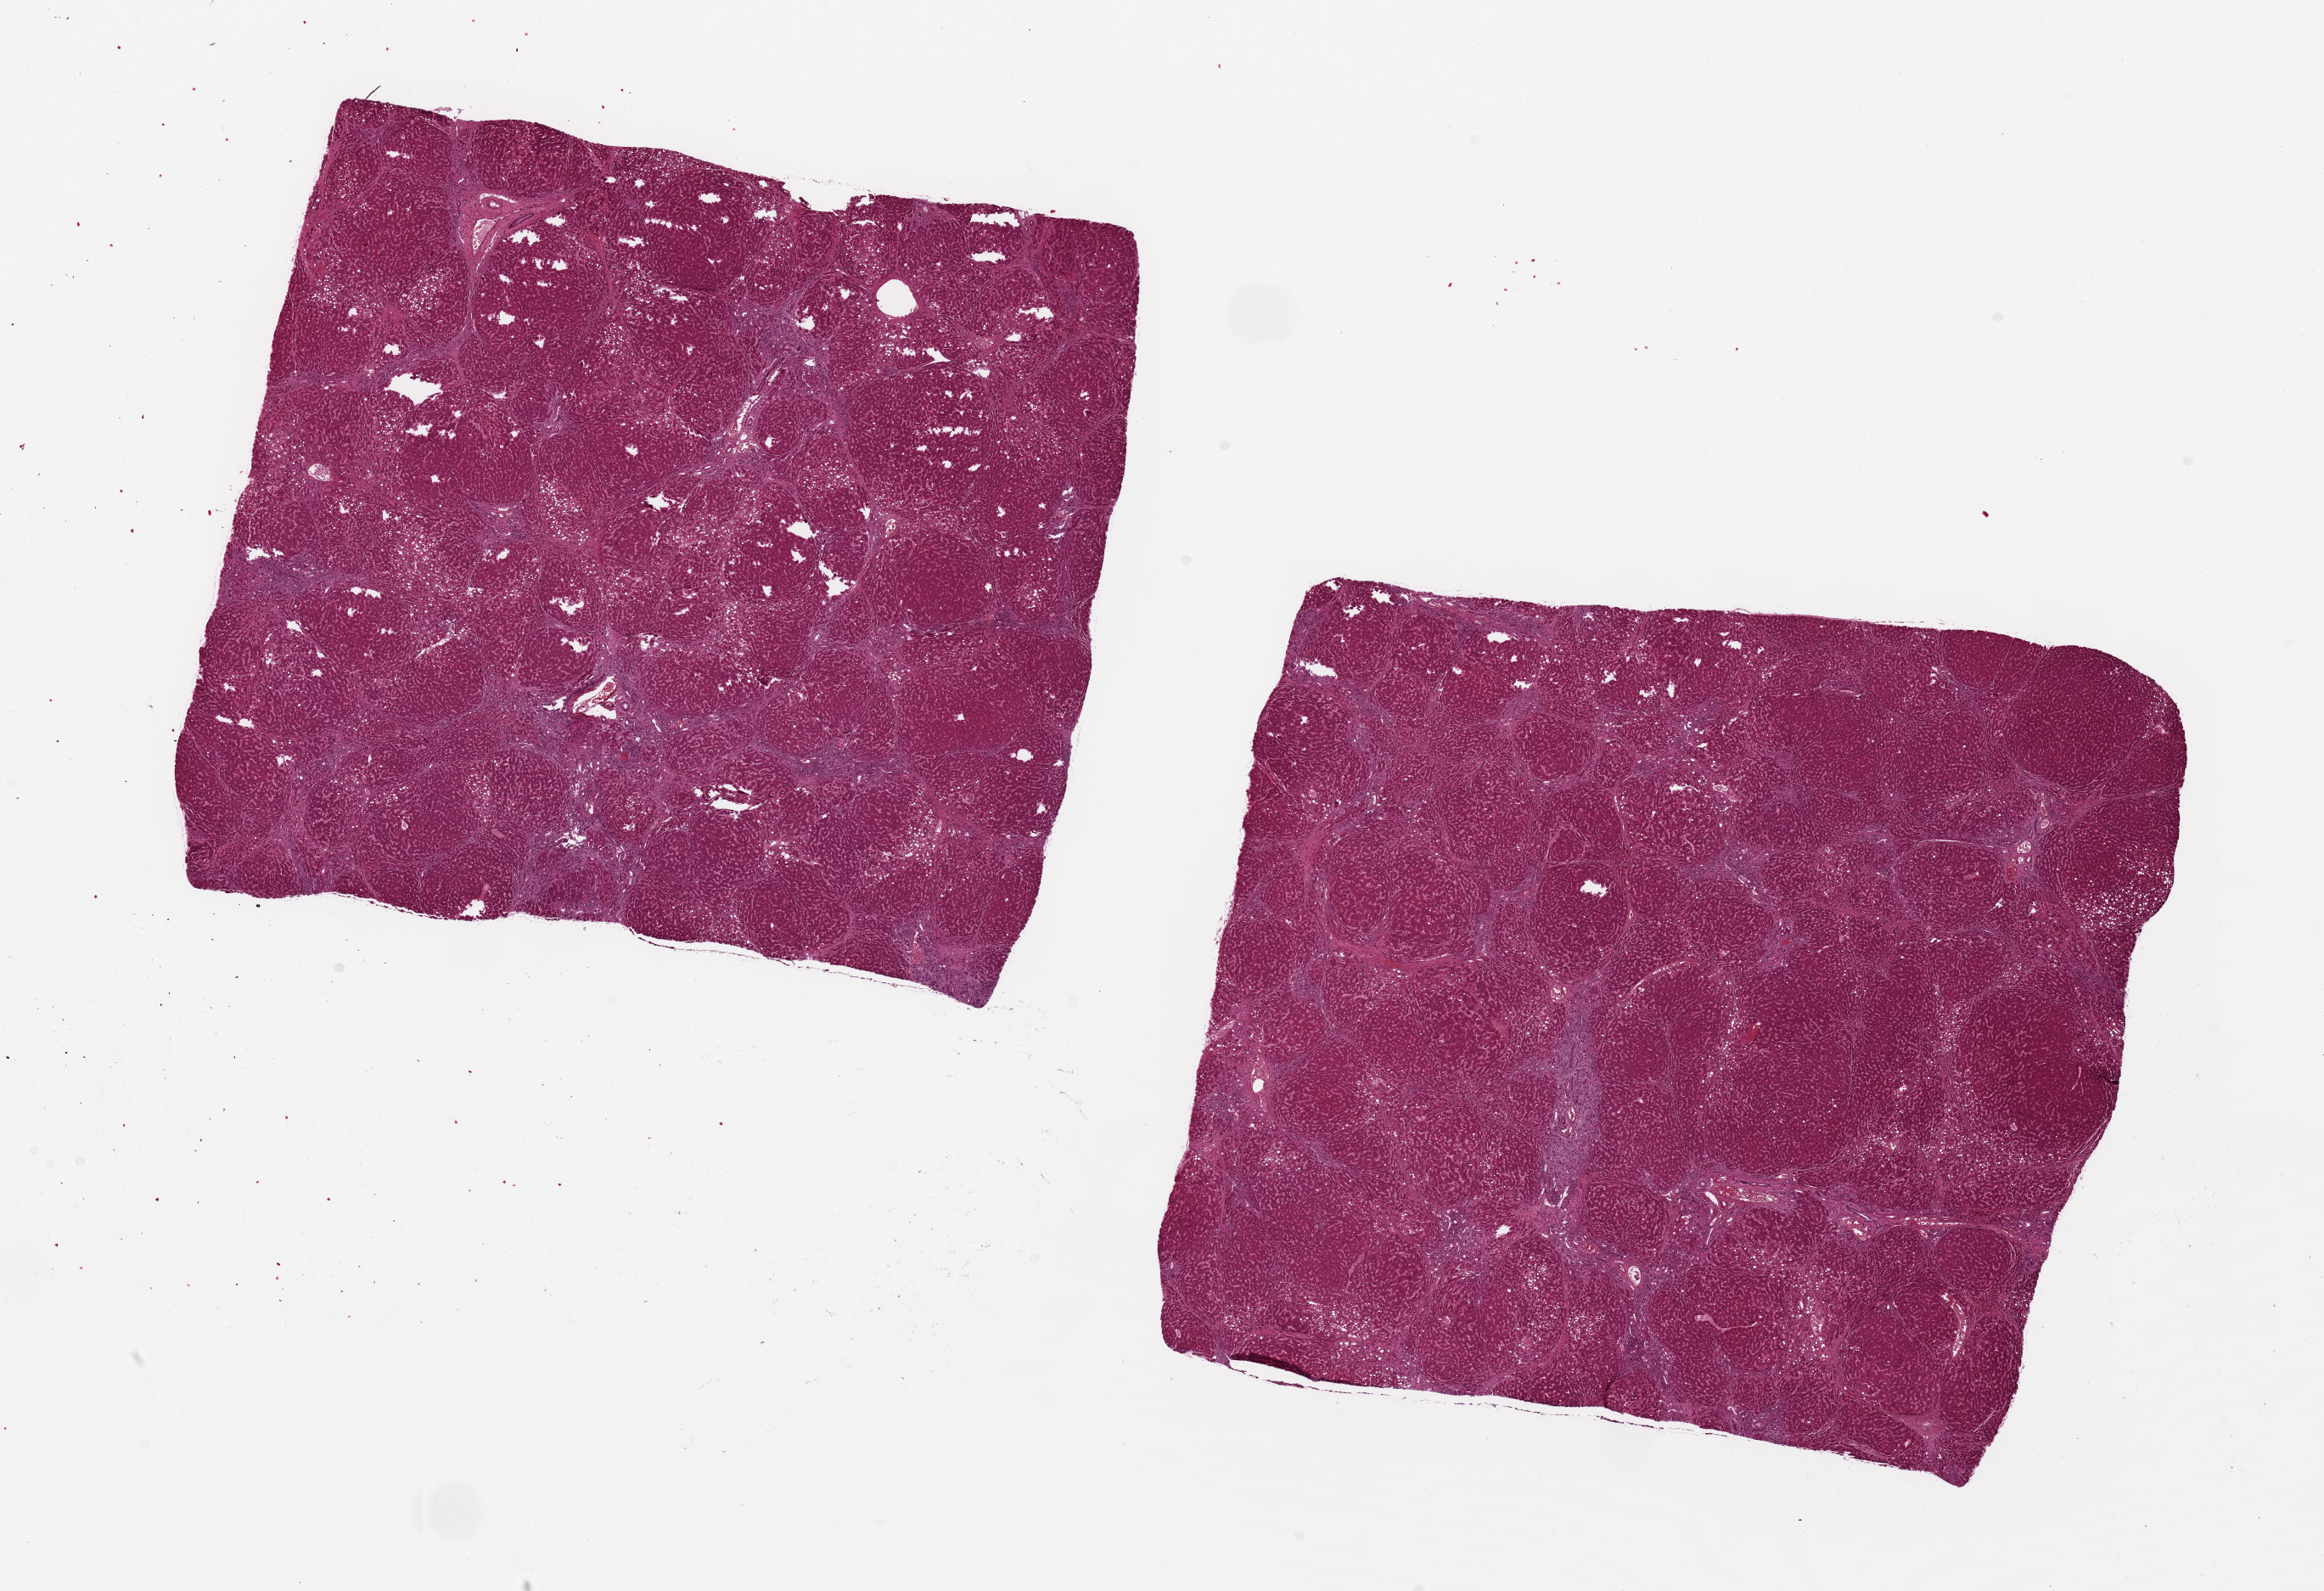
Digitized H&E-stained section, a low-resolution overview of the entire scanned area, about 21.7 x 14.8 mm (acquisition: 20x scan). PAXgene-fixed paraffin-embedded (PFPE) section. Section of liver (target tissue). Tissue donor sample. Female donor.
Review note (as recorded): 2 ~7.5x7.5mm aliquots. Severe bridging fibrosis/early cirrhosis with steatotis and chronic hepatitis.